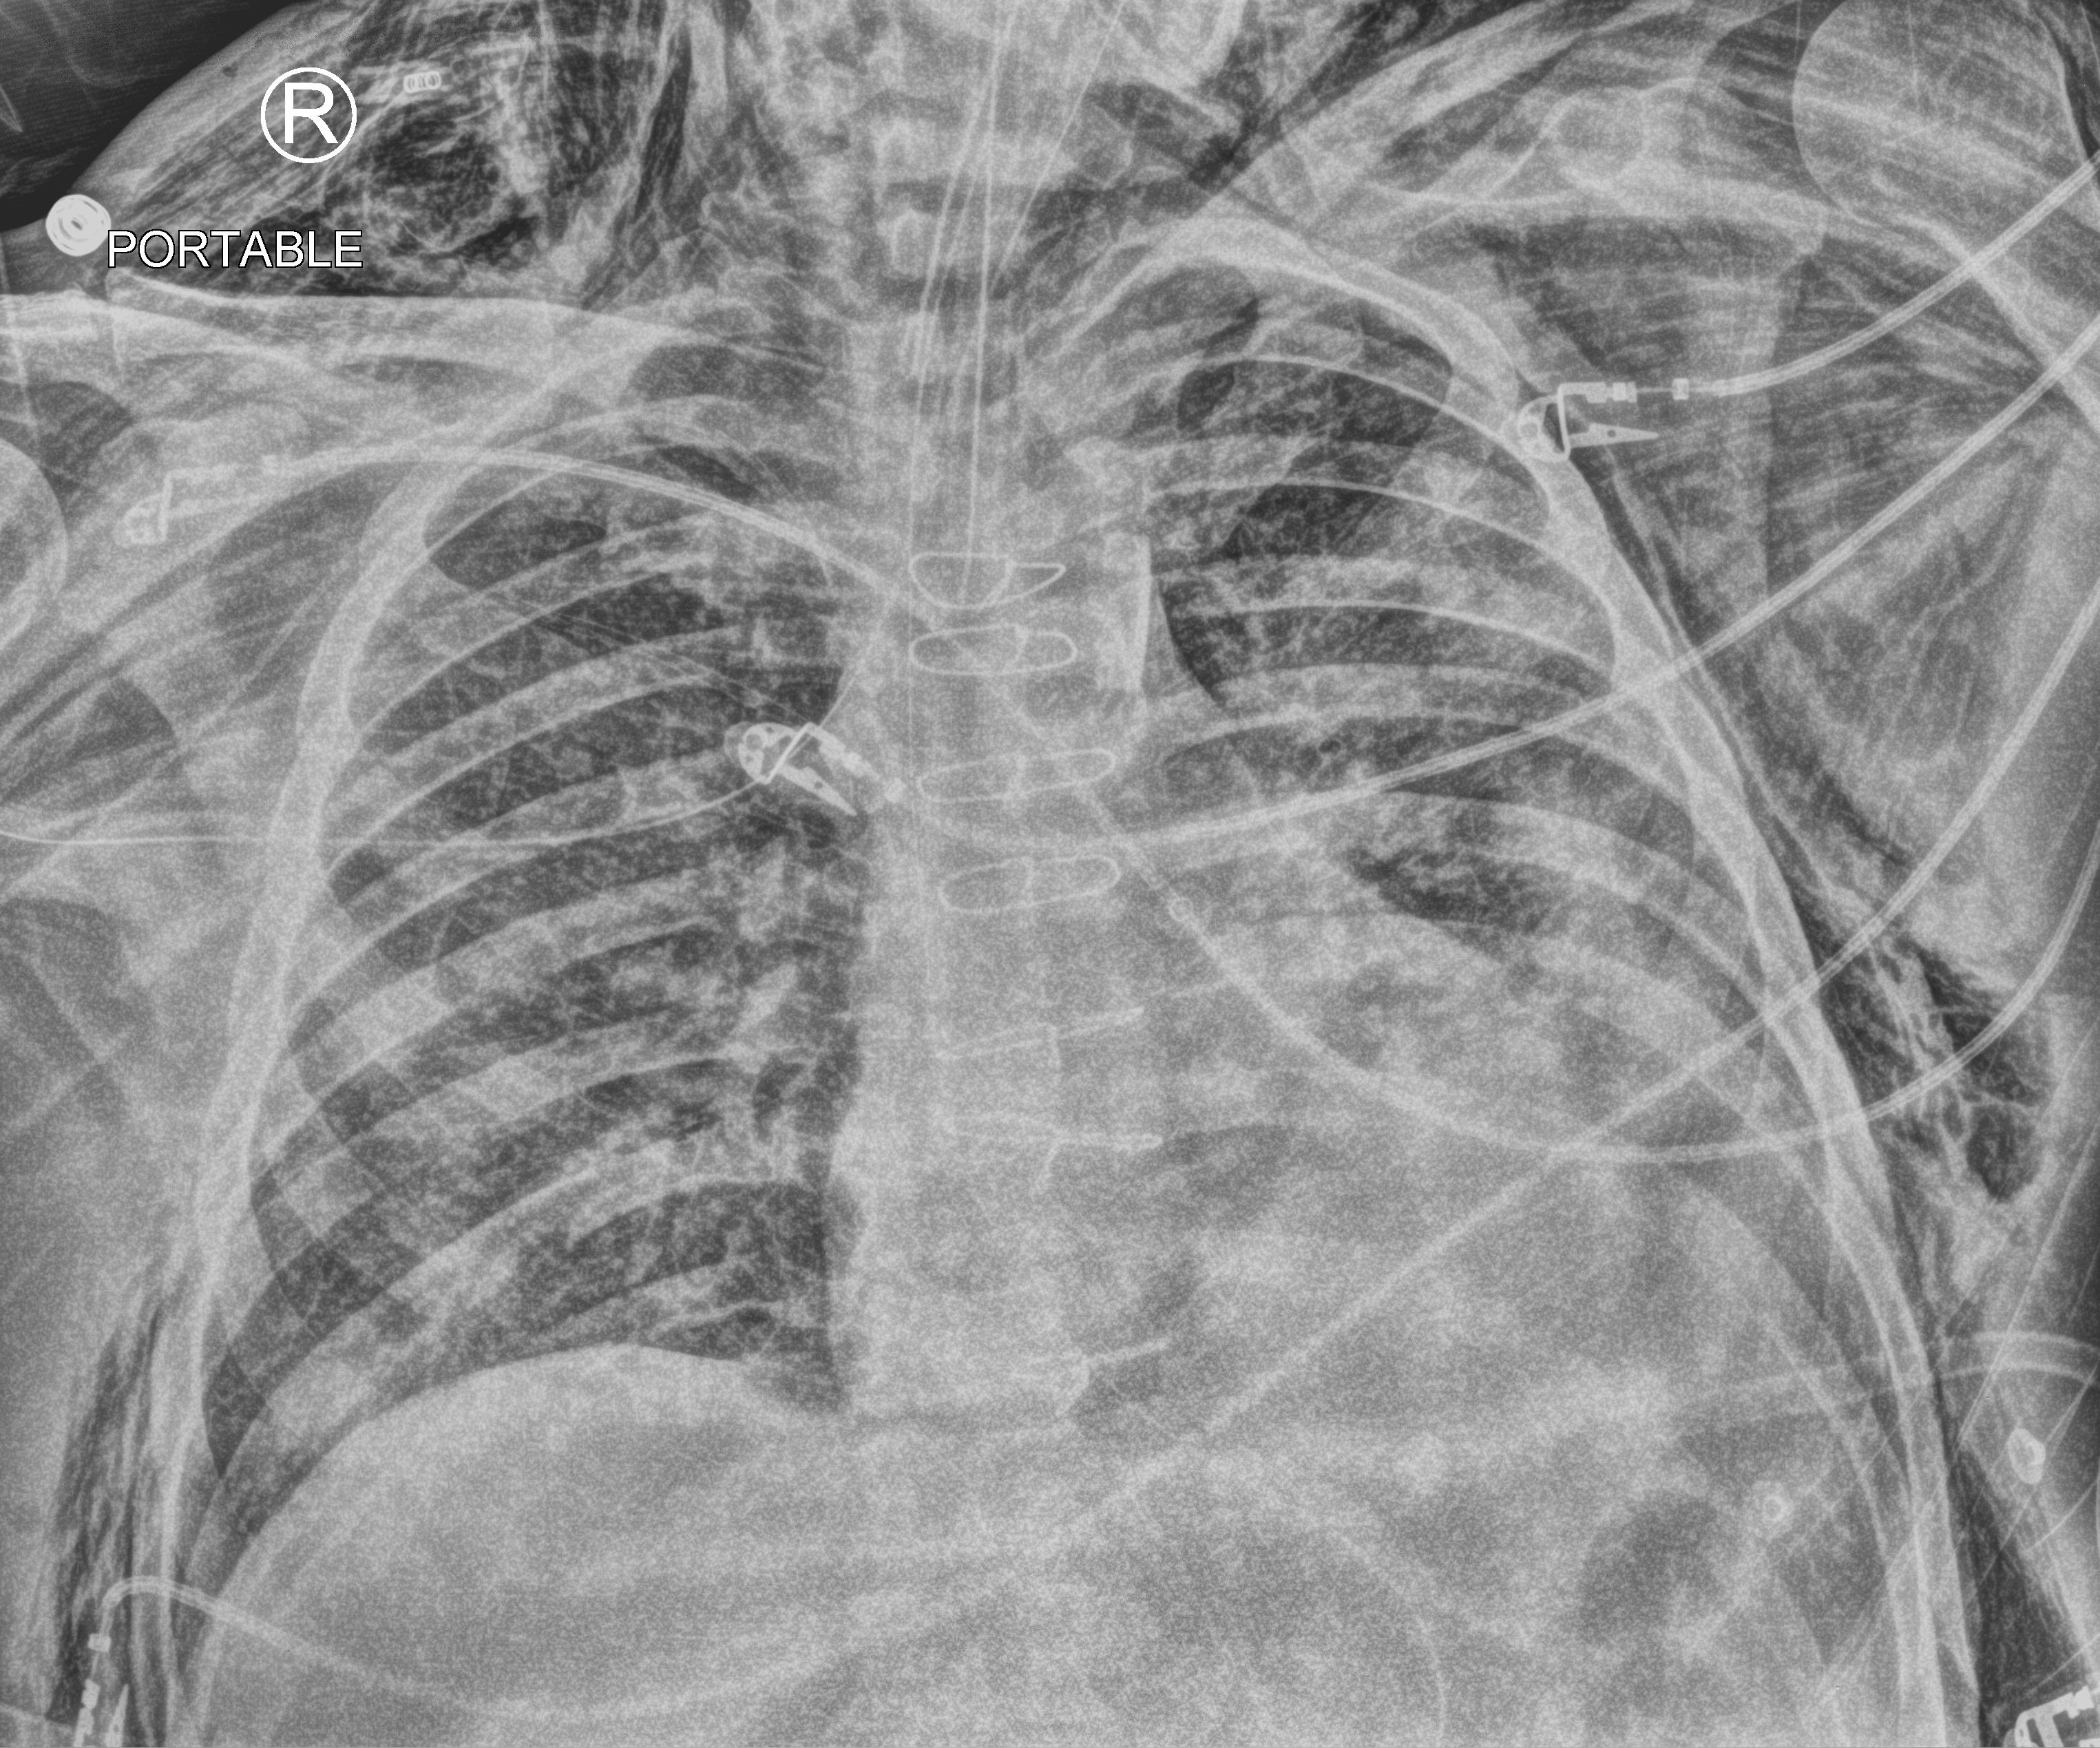
Portable chest radiograph; anteroposterior (AP) projection. Male patient hospitalised with COVID-19, age 60–74 years.
From the hospital-stay record, not from the radiograph (when in the stay this image was taken is not recorded):
- COPD (admission record): no